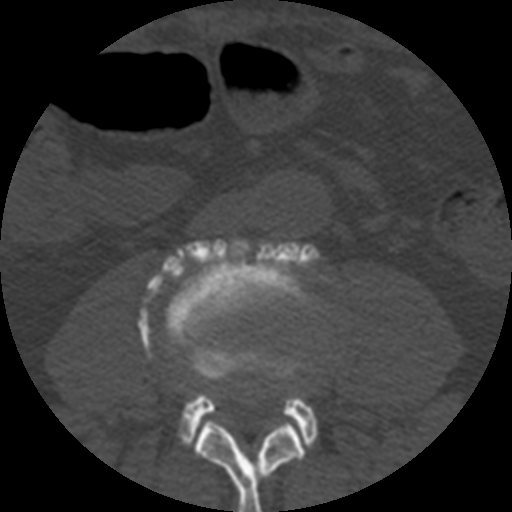
CT including the spine, one axial slice. Slice 106 of 508 in the series (ordered by position). Reconstruction kernel STANDARD. Bone window (W 1800 / L 400 HU). 1.25 mm slice thickness. 512 × 512 image matrix, field of view 160 × 160 mm. Patient age 57 years. From the clinical record (not read from this slice): primary cancer: prostate.
Annotated regions visible in this slice (semi-automatic segmentation, software-assisted and operator-edited):
- L3 vertebra: bounding box <195,421,304,512> (left, top, right, bottom; pixels)
- L4 vertebra: <138,239,320,451>